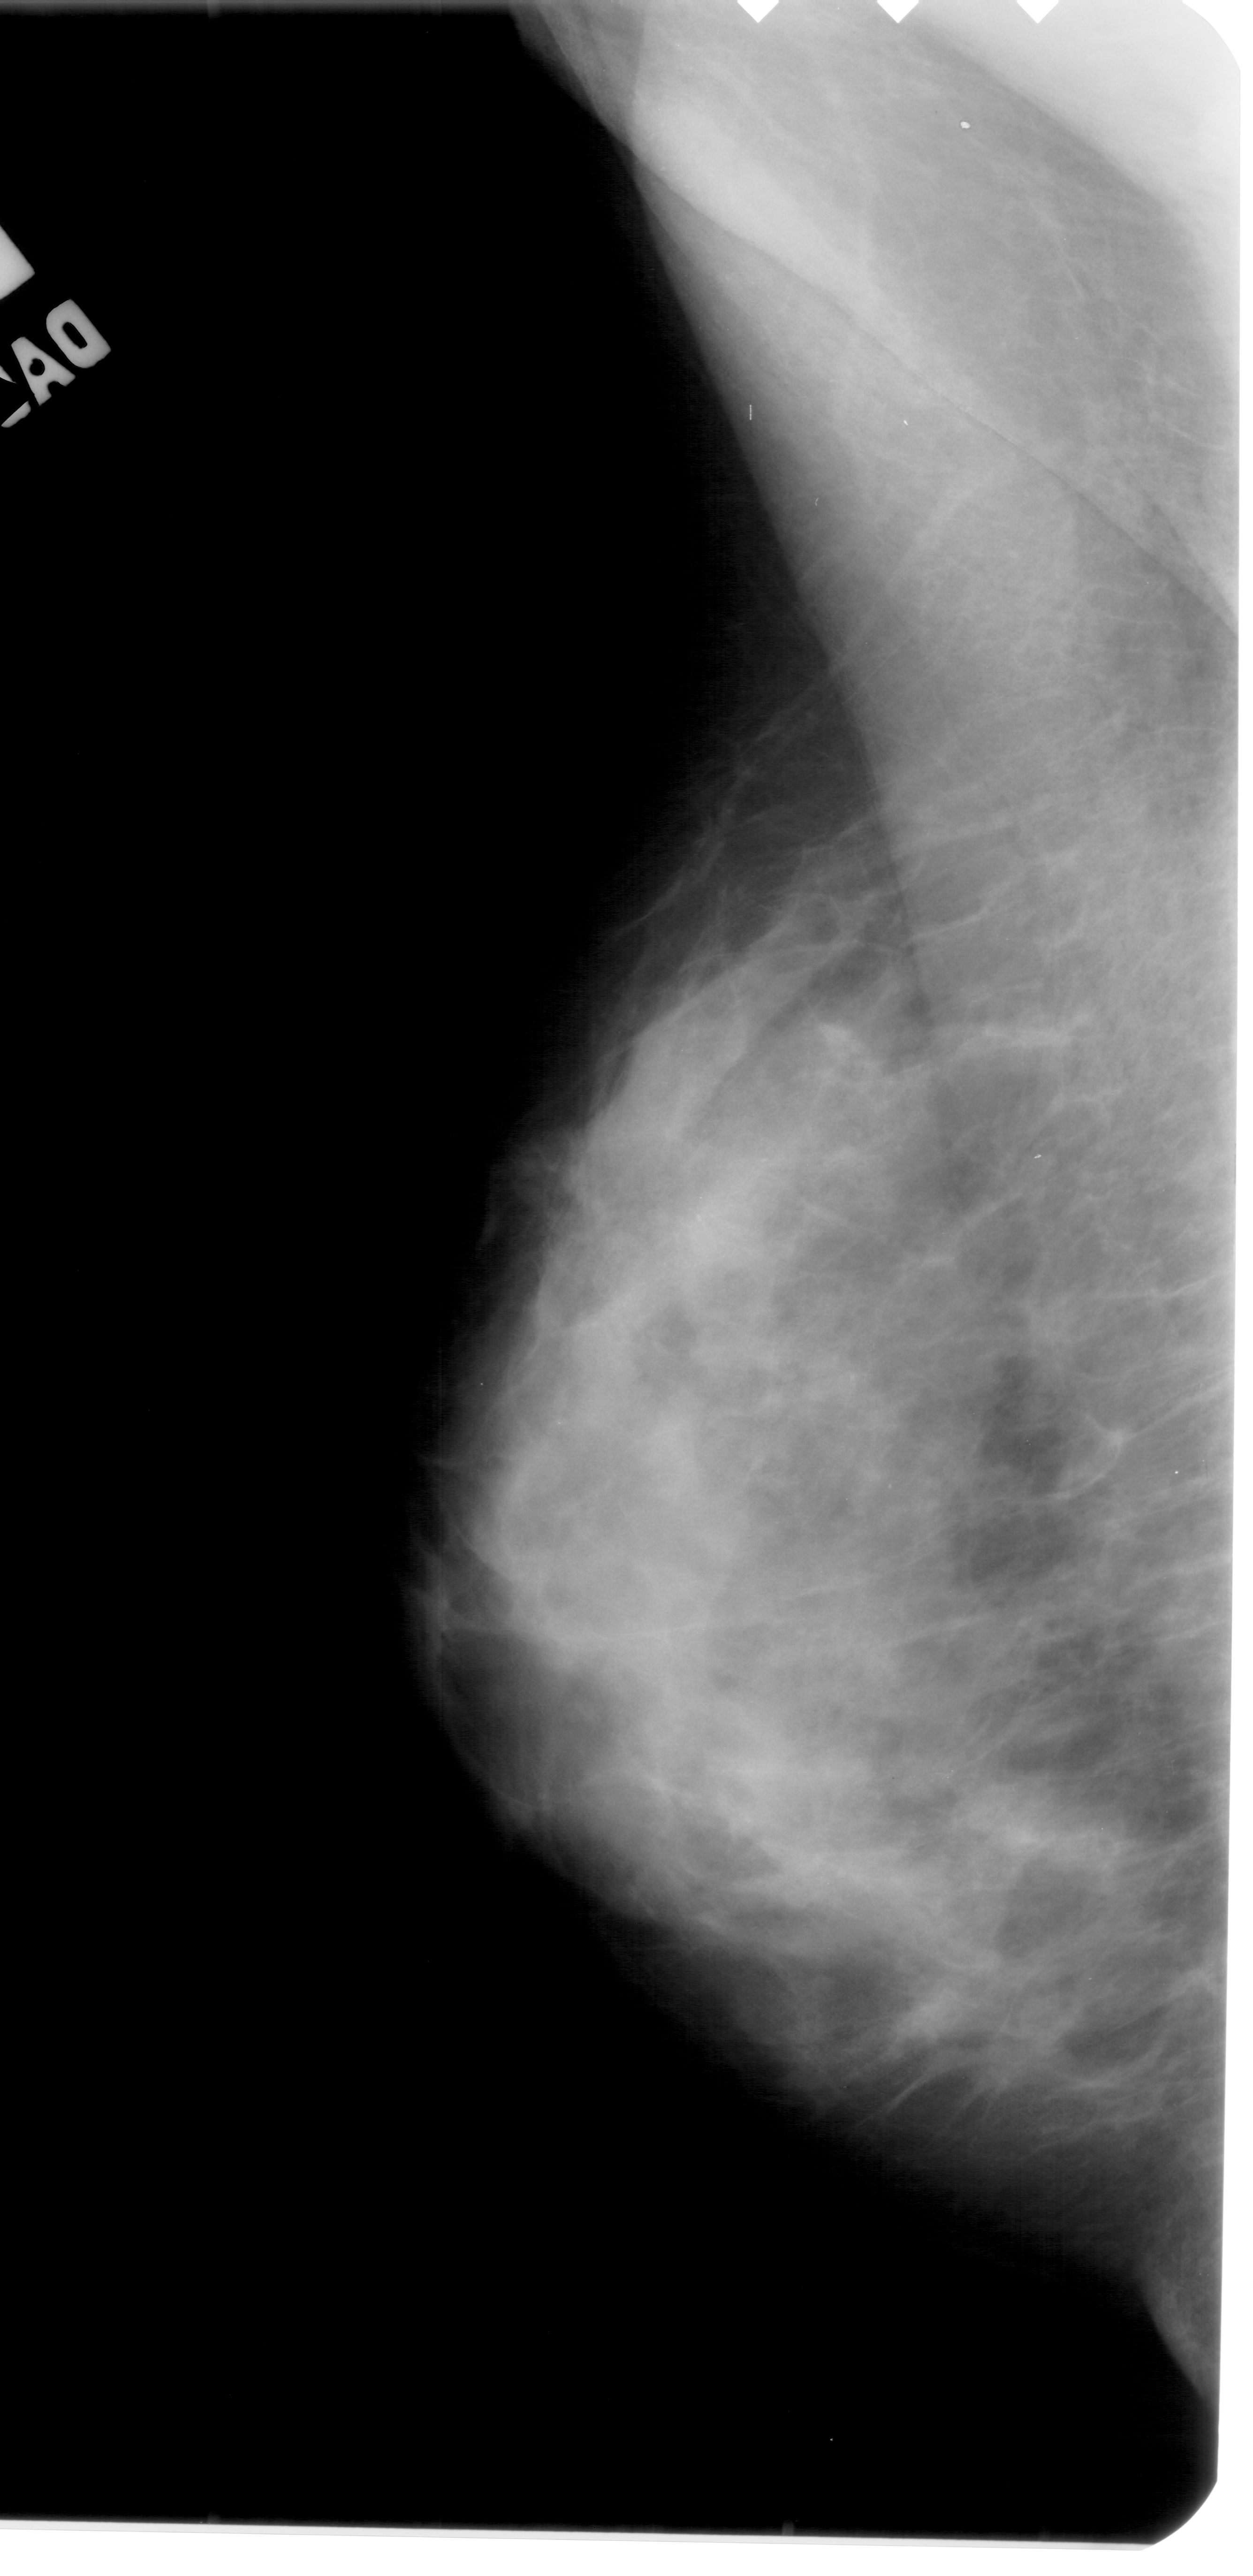
Digitized screen-film mammogram. Left breast. Mediolateral oblique (MLO) view. BI-RADS breast density category 4 (scale 1–4). 1253 × 2576 image matrix.
Marked abnormalities (boxes around the expert regions of interest):
- calcifications, morphology pleomorphic, distribution segmental; BI-RADS assessment category 4; subtlety rating 2 on a 1 (subtle) to 5 (obvious) scale; pathology (as recorded): benign: bounding box (x1, y1, x2, y2) in pixels: (617, 1135, 780, 1335)